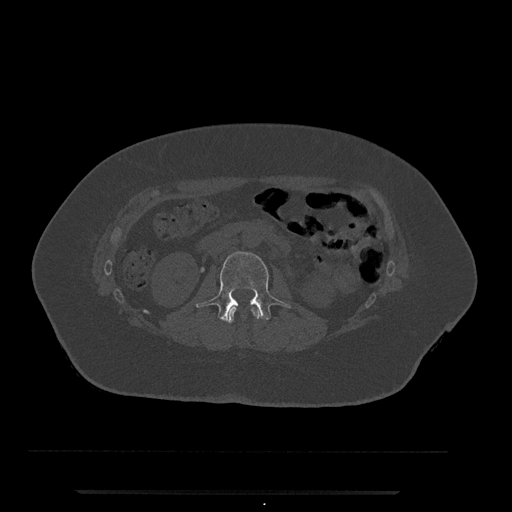
CT including the spine, one axial slice; position 47 of 797 along the scan axis; bone window (W 1800 / L 400 HU); 0.5 mm slice thickness; 512 × 512 image matrix, field of view 440 × 440 mm. Female patient, age 51 years. Case-level facts recorded for this patient, not image findings: primary cancer: neuro.
Annotated regions visible in this slice (semi-automatic segmentation, software-assisted and operator-edited):
- L1 vertebra: bounding box [x1, y1, x2, y2] px = [227, 307, 261, 323]
- L2 vertebra: [196, 251, 291, 322]